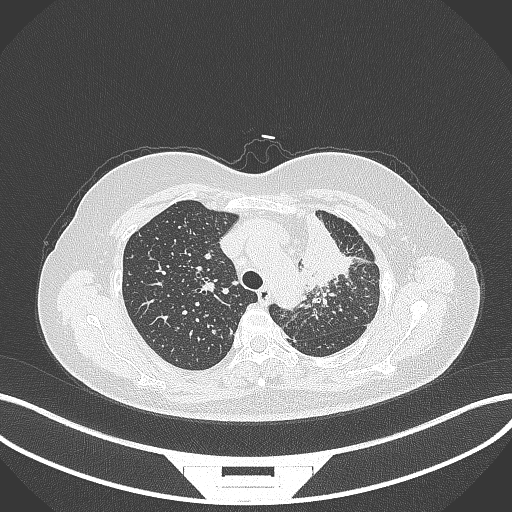
Chest CT, one axial slice. Position 253 of 348 along the scan axis. Reconstruction kernel B70f. 120 kVp. Lung window (W 1500 / L -600 HU). 1 mm slice thickness. 512 × 512 image matrix, field of view 400 × 400 mm. Patient: female, 49 years. Case-level facts recorded for this patient, not image findings: clinical TNM (as recorded): T1c N0 M1.
Outlined on this slice (rectangle marked by the reading radiologist):
- lung tumour (recorded histology: adenocarcinoma): bounding box <294,211,353,293> (left, top, right, bottom; pixels)